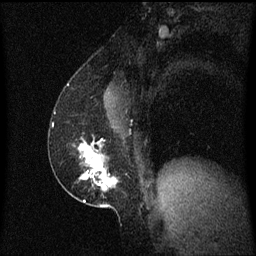
Breast MRI (dynamic contrast-enhanced), one sagittal slice. Position 34 of 60 along the scan axis. Dynamic contrast-enhanced series, image 2 of 3 at this slice position (ordered by acquisition). 1.5 T. TE 4.2 ms, TR 8.4 ms. 2 mm slice thickness. 256 × 256 image matrix. Patient: female, 52 years. Case-level facts recorded for this patient, not image findings: setting: breast cancer imaged before/during neoadjuvant chemotherapy; receptor status: HER2-positive.
Annotated regions visible in this slice (semi-automatically segmented with operator editing):
- analysis volume of interest (the breast-tissue region the enhancement analysis was run in; not a lesion): bounding box <62,136,119,203> (left, top, right, bottom; pixels)
- tumour enhancement mask (voxels above the 70 % enhancement threshold inside the analysis volume of interest): <79,142,119,191>